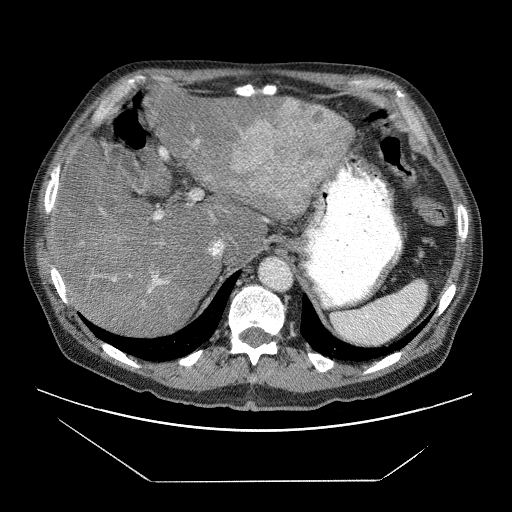
Contrast-enhanced abdominal CT (liver protocol), one axial slice. Slice 50 of 83 in the series (ordered by position). 120 kVp. Soft-tissue window (W 400 / L 40 HU). 2.5 mm slice thickness. 512 × 512 image matrix. Case-level facts recorded for this patient, not image findings: diagnosis: hepatocellular carcinoma (patient treated with transarterial chemoembolisation; whether this scan precedes or follows treatment is not stated here); TNM stage (as recorded): Stage-IVB; Child-Pugh class: B; tumour differentiation: poorly differentiated; tumour nodularity: uninodular.
Structures marked on this image (semi-automatically segmented with operator editing):
- liver parenchyma outside the tumour (the mass and vessels are separate outlines, so this box may not span the whole liver): bounding box (x1, y1, x2, y2) in pixels: (48, 82, 354, 336)
- mass: (232, 99, 352, 216)
- liver vessels: (100, 93, 271, 305)